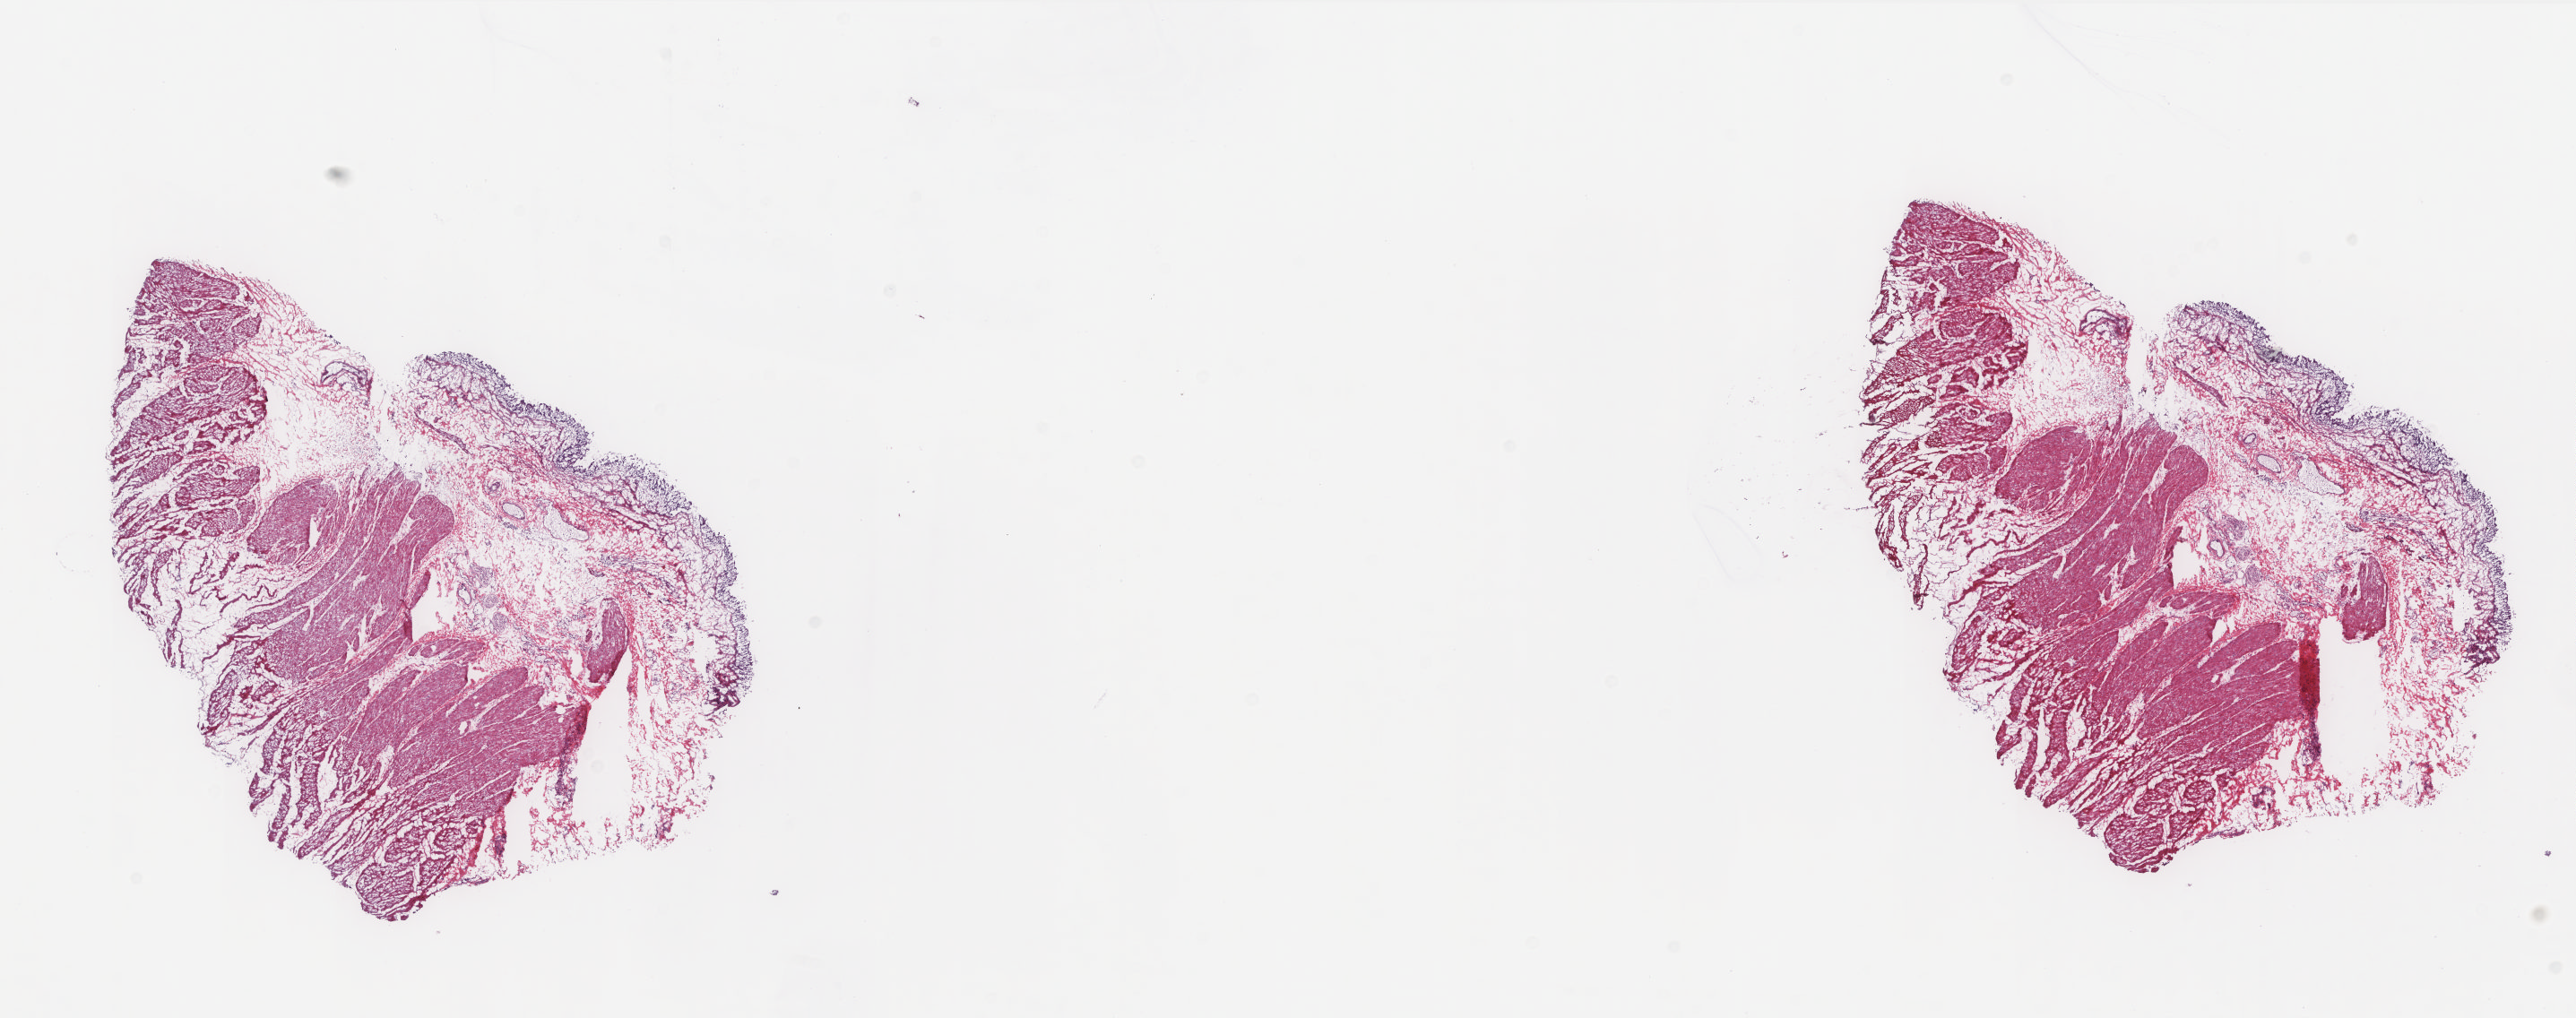
Whole-slide histology image, H&E — a low-resolution overview of the entire scanned area, about 23.0 x 9.1 mm (slide scanned at 20x), frozen section, solid tissue normal (non-tumour tissue) sample from the bladder. Patient: male, age at initial diagnosis 48 years. Composition of this section per pathologist review: tumour cells 0%, tumour nuclei 0%, normal cells 10%, stromal cells 90%, necrosis 0%. Infiltration values recorded for this section: lymphocyte infiltration 0%, monocyte infiltration 0%, neutrophil infiltration 0%.
- this section: solid tissue normal (non-tumour) sample from the same patient
- patient diagnosis: Transitional cell carcinoma